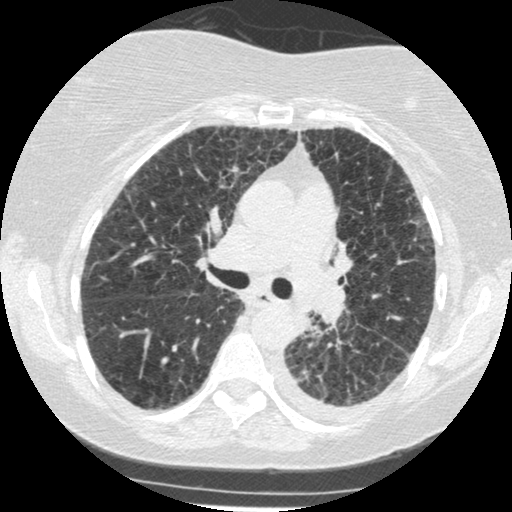
Low-dose screening chest CT, one axial slice; slice 167 of 341 in the series (ordered by position); 120 kVp; lung window (W 1500 / L -600 HU); 1.25 mm slice thickness; 512 × 512 image matrix.
Structures marked on this image (outlined manually by an expert reader):
- lesion 1 (tumor, lower lobe of left lung): box from (x=297, y=311) to (x=311, y=332) px